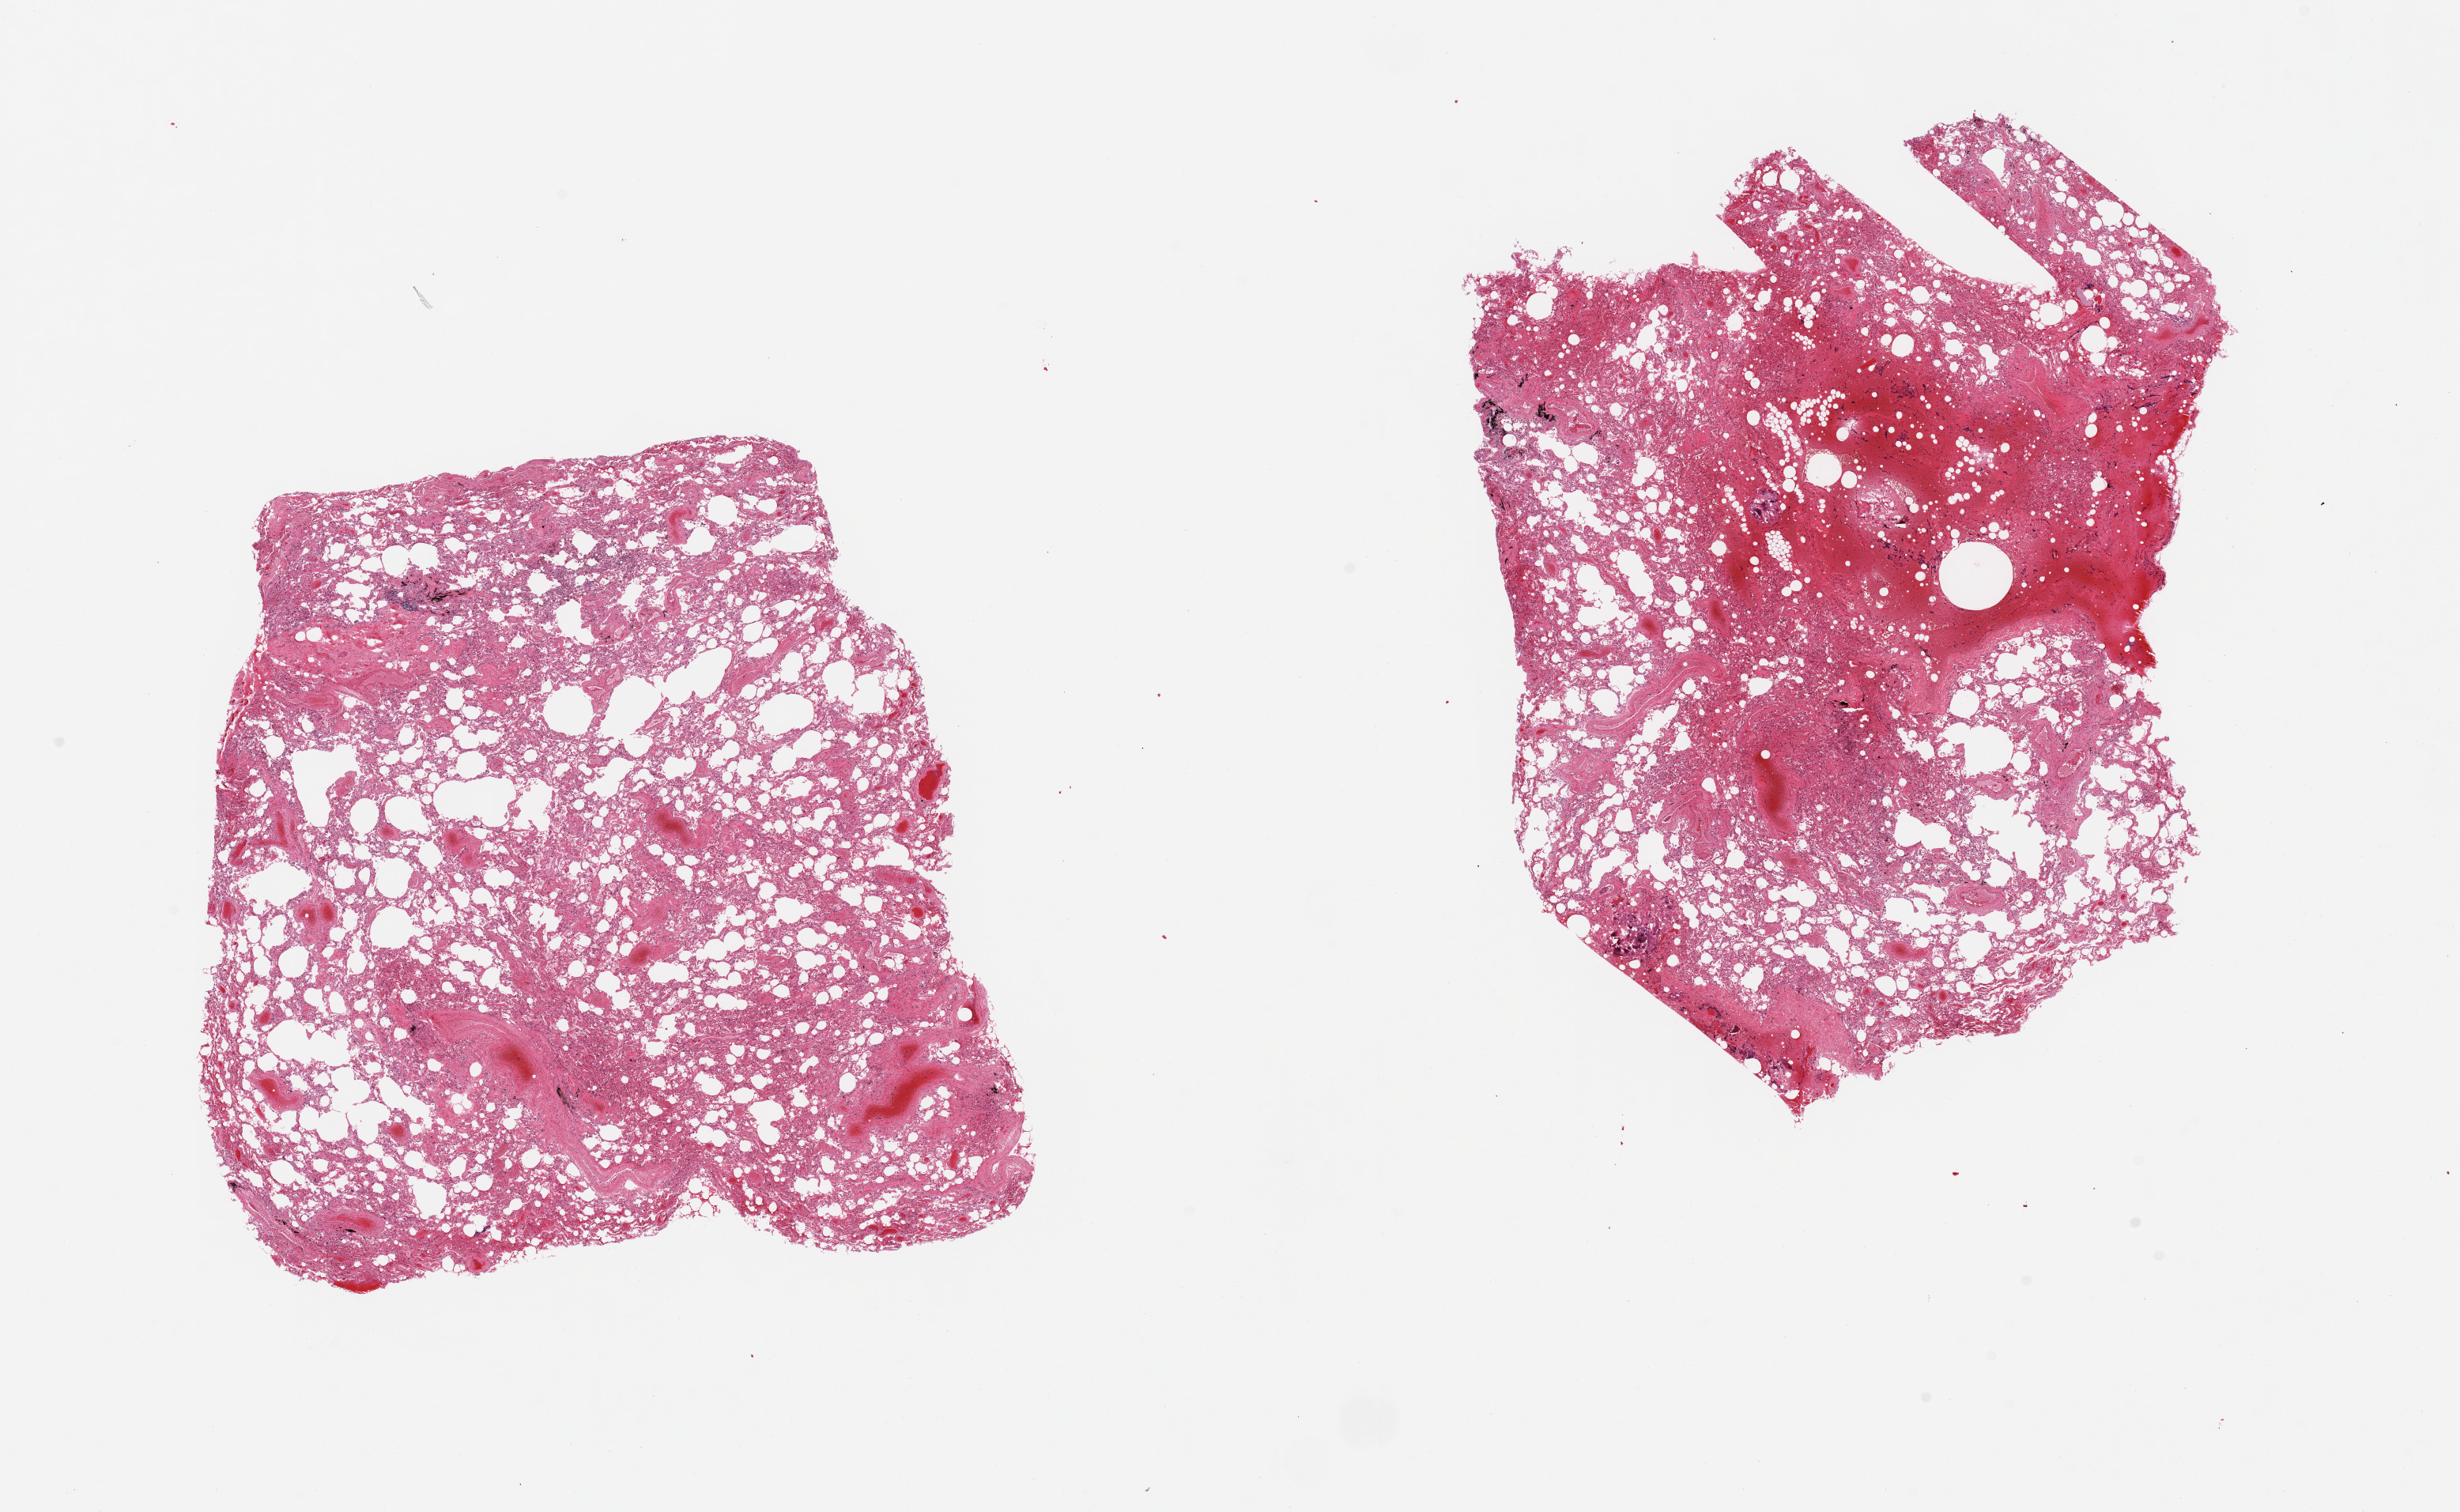
Whole-slide image, haematoxylin and eosin stain, low-resolution overview of the scanned area, about 24.6 x 15.1 mm (from a 20x scan), PAXgene-fixed, paraffin-embedded tissue, target tissue: lung, tissue donor sample. Male donor.
Review note (as recorded): 2 pieces, some hemosiderin-laden macrophages, emphysematous change, area of hemorrhage and foci of calcified material, isolated fragment of skeletal muscle (? aspiration).